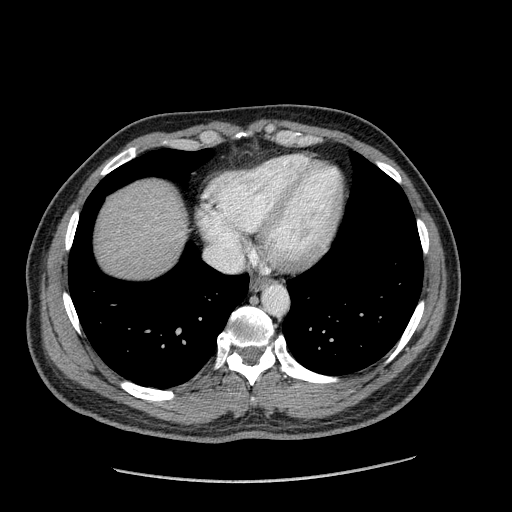
Contrast-enhanced abdominal CT (liver protocol), one axial slice. Position 167 of 182 along the scan axis. 120 kVp. Soft-tissue window (W 400 / L 40 HU). 2.5 mm slice thickness. 512 × 512 image matrix, field of view 400 × 400 mm. From the clinical record (not read from this slice): diagnosis: hepatocellular carcinoma (patient treated with transarterial chemoembolisation; whether this scan precedes or follows treatment is not stated here); TNM stage (as recorded): Stage-I; Child-Pugh class: A; tumour differentiation: well differentiated; tumour nodularity: uninodular.
Structures marked on this image (semi-automatic segmentation, software-assisted and operator-edited):
- abdominal aorta: box from (x=262, y=286) to (x=287, y=315) px
- liver parenchyma outside the tumour (the mass and vessels are separate outlines, so this box may not span the whole liver): (x=96, y=180)–(x=186, y=278)